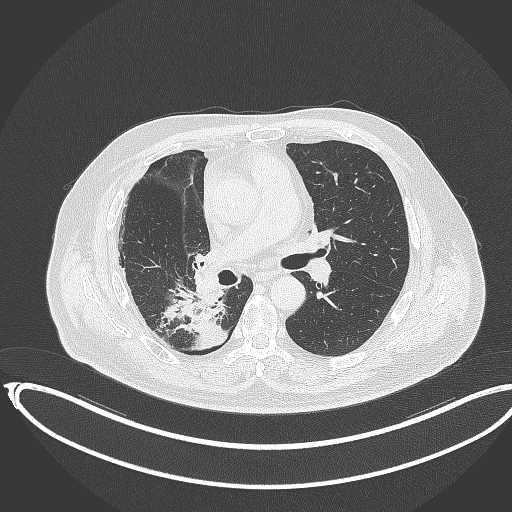
Chest CT, one axial slice; slice 195 of 403 in the series (ordered by position); reconstruction kernel B70f; lung window (W 1500 / L -600 HU); 512 × 512 image matrix, field of view 436 × 436 mm. Male patient, age 68 years. From the clinical record (not read from this slice): clinical TNM (as recorded): T2a N0 M0.
Annotated regions visible in this slice (bounding box drawn by a radiologist):
- lung tumour (recorded histology: adenocarcinoma): bounding box [x1, y1, x2, y2] px = [153, 288, 229, 354]